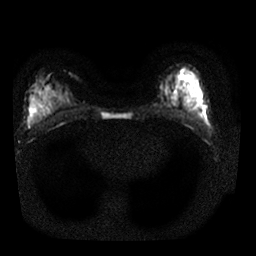
Breast MRI, one axial slice; slice 10 of 25 in the series (ordered by position); diffusion-weighted series; image 2 of 4 stored at this slice position (different b-values; order by instance number); 1.5 T; 4 mm slice thickness; 256 × 256 image matrix, field of view 320 × 320 mm. Female patient.
Outlined on this slice (expert manual segmentation):
- tumour on diffusion-weighted imaging: bounding box <190,104,196,109> (left, top, right, bottom; pixels)